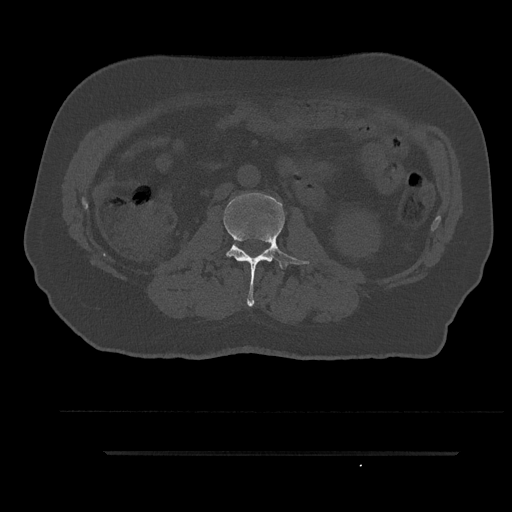
CT including the spine, one axial slice; slice 103 of 797 in the series (ordered by position); 120 kVp; bone window (W 1800 / L 400 HU); 0.5 mm slice thickness; 512 × 512 image matrix, field of view 432 × 432 mm. Male patient, age 63 years. From the clinical record (not read from this slice): primary cancer: renal; vertebrae with lytic lesions (as recorded): T8.
Annotated regions visible in this slice (semi-automatically segmented with operator editing):
- L2 vertebra: box from (x=224, y=193) to (x=310, y=306) px